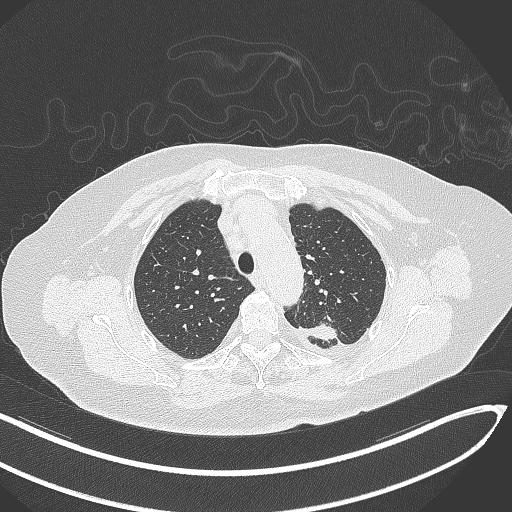
Chest CT, one axial slice; 120 kVp; lung window (W 1500 / L -600 HU); 512 × 512 image matrix, field of view 400 × 400 mm. Female patient, age 76 years. Case-level facts recorded for this patient, not image findings: clinical TNM (as recorded): T1c N0 M0.
Structures marked on this image (rectangle marked by the reading radiologist):
- lung tumour (recorded histology: adenocarcinoma): bounding box [x1, y1, x2, y2] px = [292, 316, 344, 349]